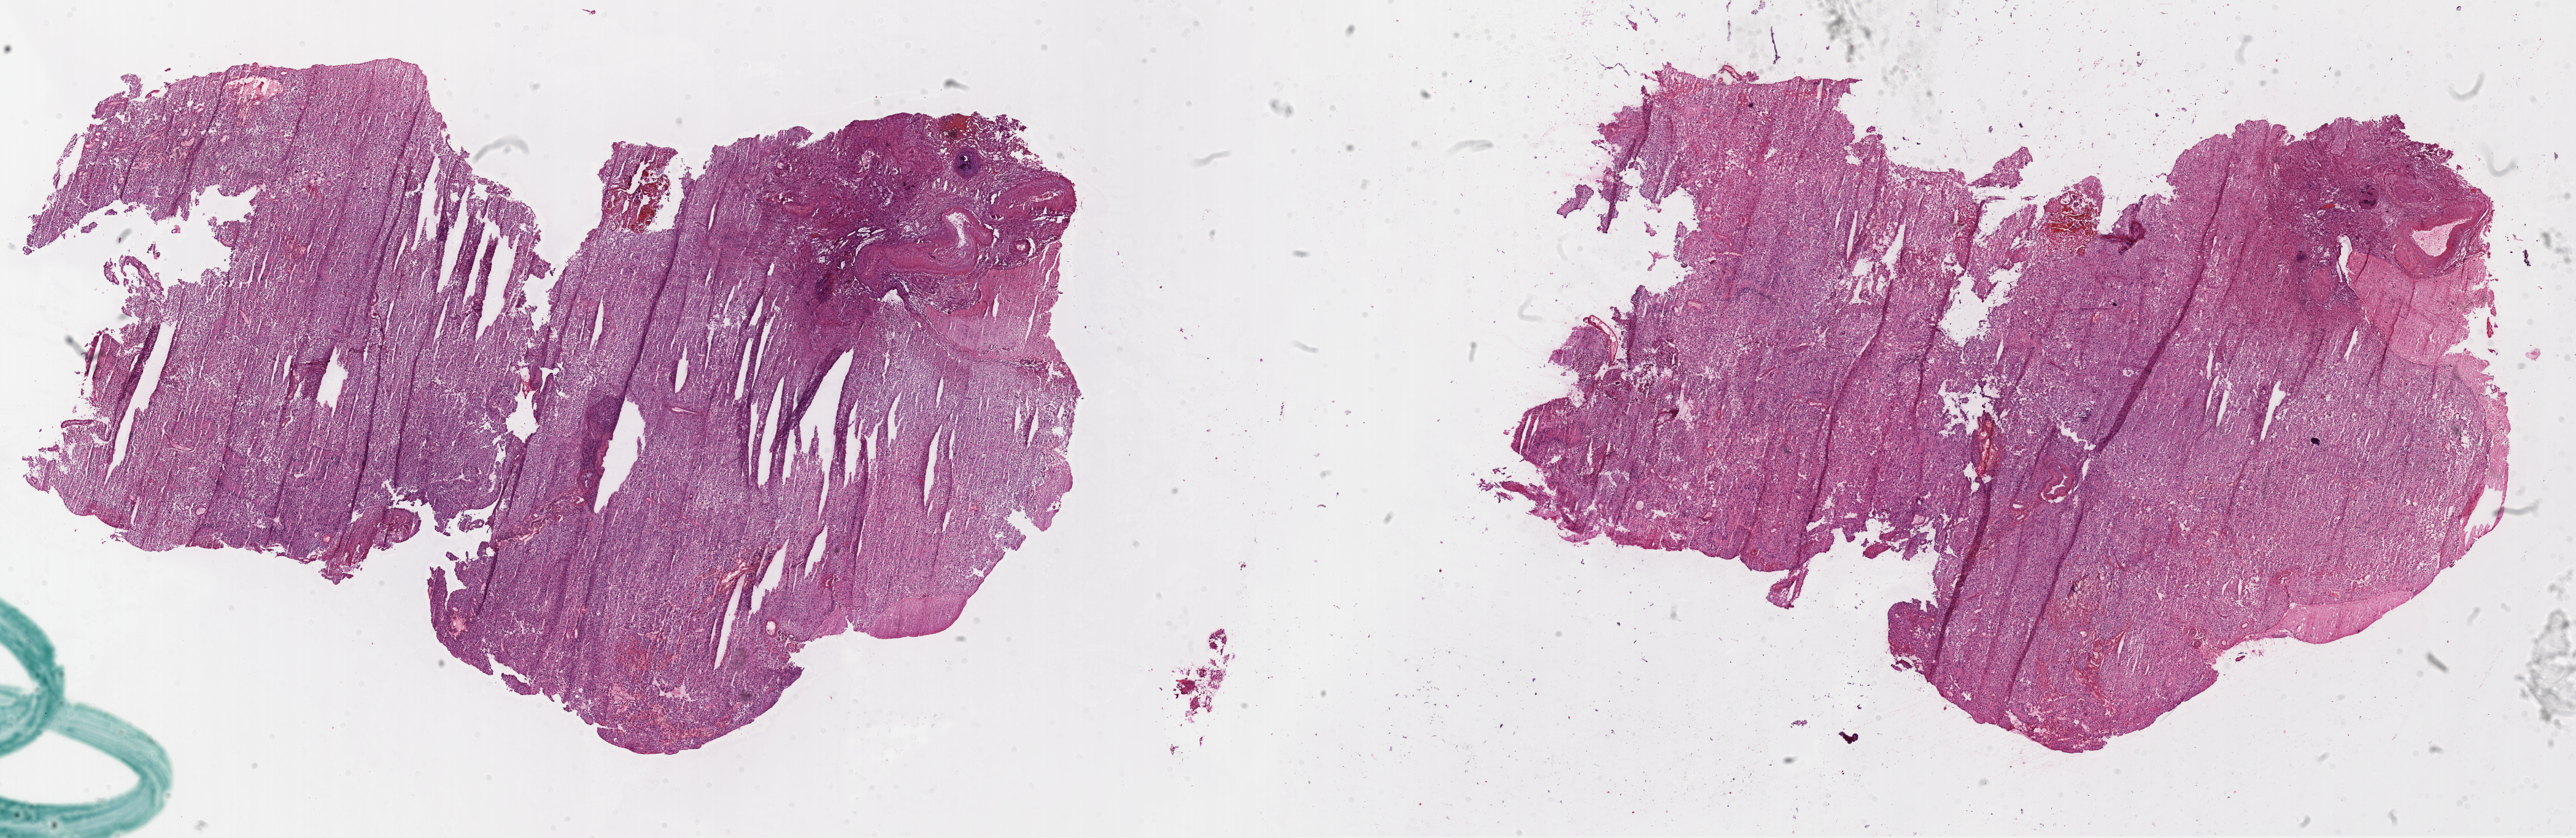
Digitized H&E-stained tissue section (whole slide) — low-resolution overview of the scanned area, about 33.8 x 11.0 mm; frozen section; primary tumour sample from the brain. Female patient; age at initial diagnosis 43 years. Pathologist review of this section (percent, as recorded): tumour cells 90%, tumour nuclei 95%, normal cells 0%, stromal cells 5%, necrosis 5%.
Pathologic diagnosis: Glioblastoma.